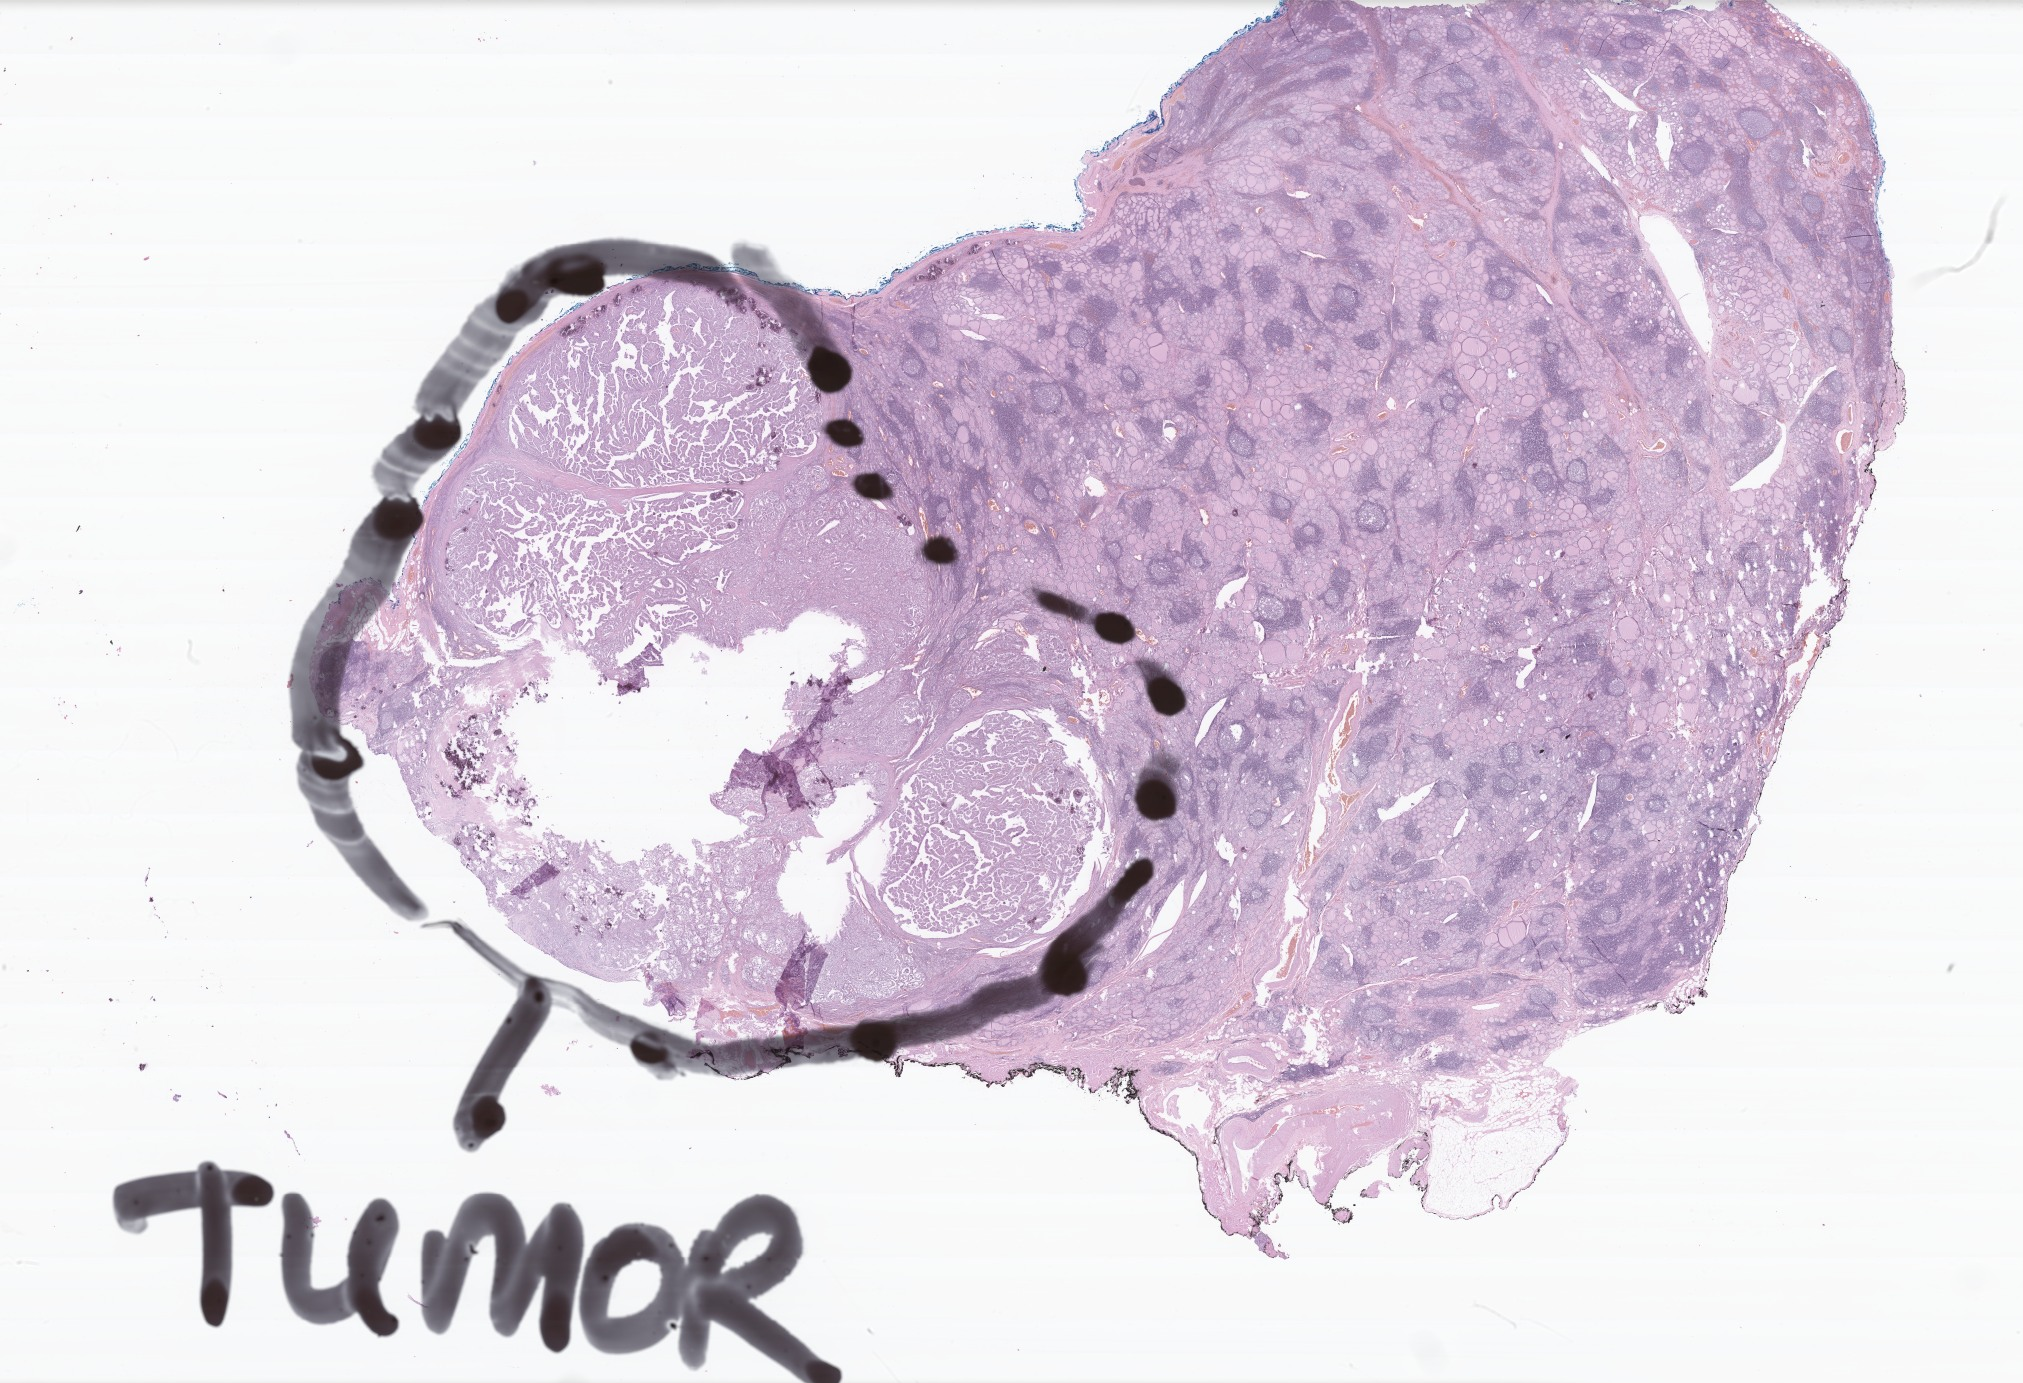
Haematoxylin and eosin whole-slide image of tumor tissue from the thyroid — low-resolution overview of the scanned area, about 34.0 x 23.3 mm, FFPE section. Female patient, age 208 months.
Diagnosis: Papillary carcinoma, NOS.